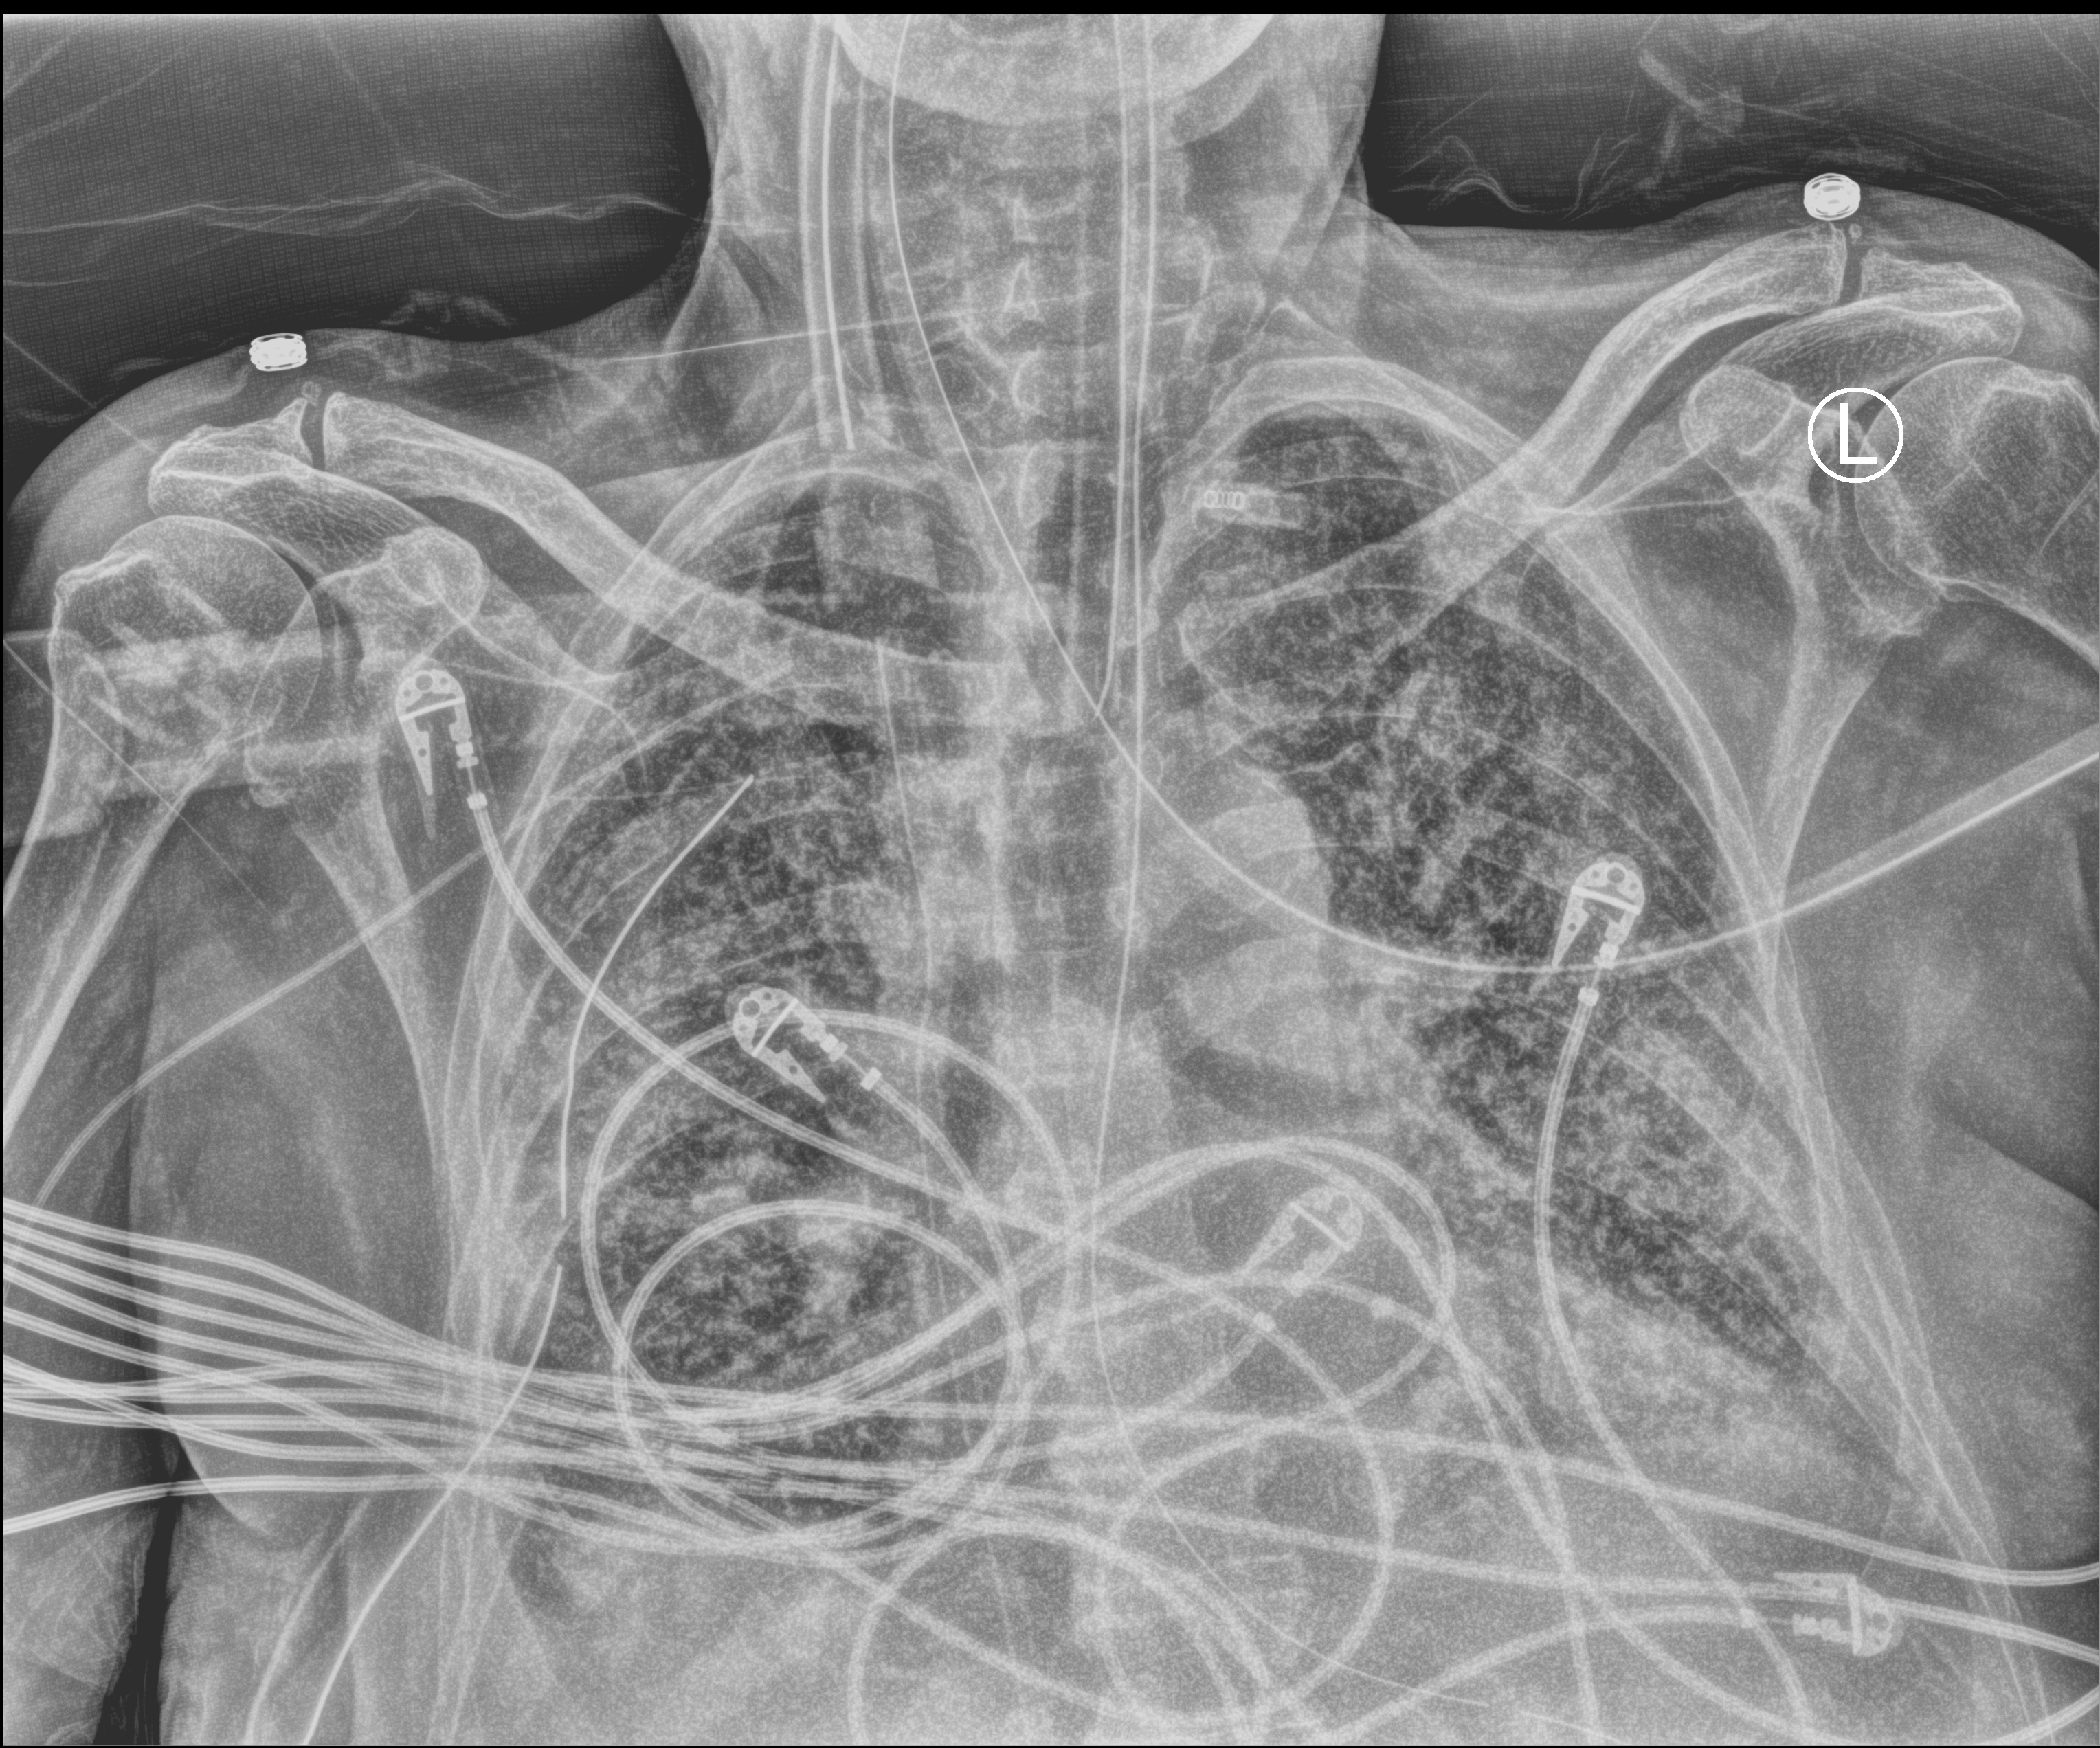
Chest X-ray (portable), anteroposterior (AP) projection. Male patient hospitalised with COVID-19, age 75–90 years.
Hospital-stay facts (about this admission, not read from this image; timing relative to this image not recorded): length of hospital stay: 47 days; admitted to intensive care during this hospital stay: yes.